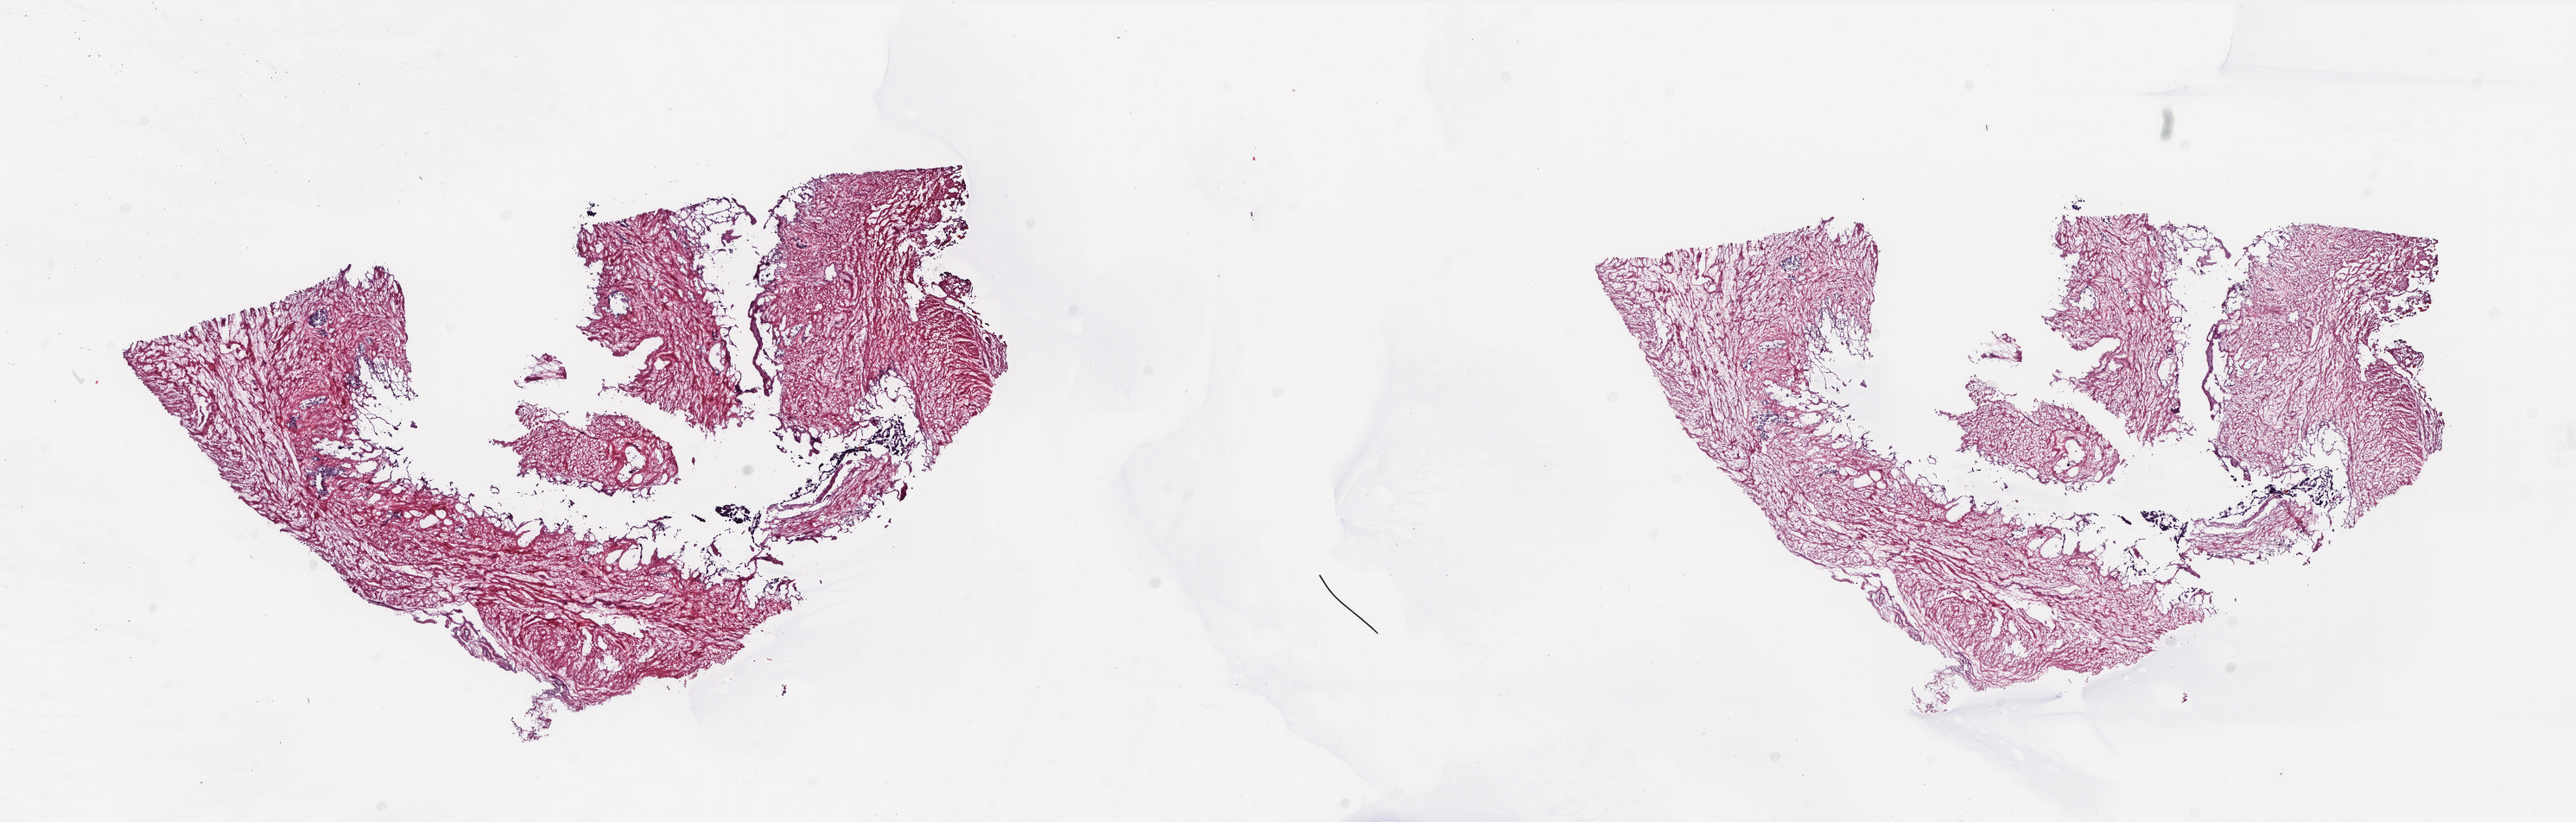
H&E-stained whole-slide image, shown as a low-resolution overview of the whole scanned area (about 24.0 x 7.7 mm, slide scanned at 20x), frozen section, solid tissue normal (non-tumour tissue) sample from the prostate. Patient: male, age at initial diagnosis 66 years. Slide review estimates, as recorded: tumour cells 0%, tumour nuclei 0%, normal cells 10%, stromal cells 90%, necrosis 0%. Infiltration values recorded for this section: lymphocyte infiltration 0%, monocyte infiltration 0%, neutrophil infiltration 0%.
This section: solid tissue normal (non-tumour) sample from the same patient. Patient diagnosis: Adenocarcinoma, NOS (prostate gland).